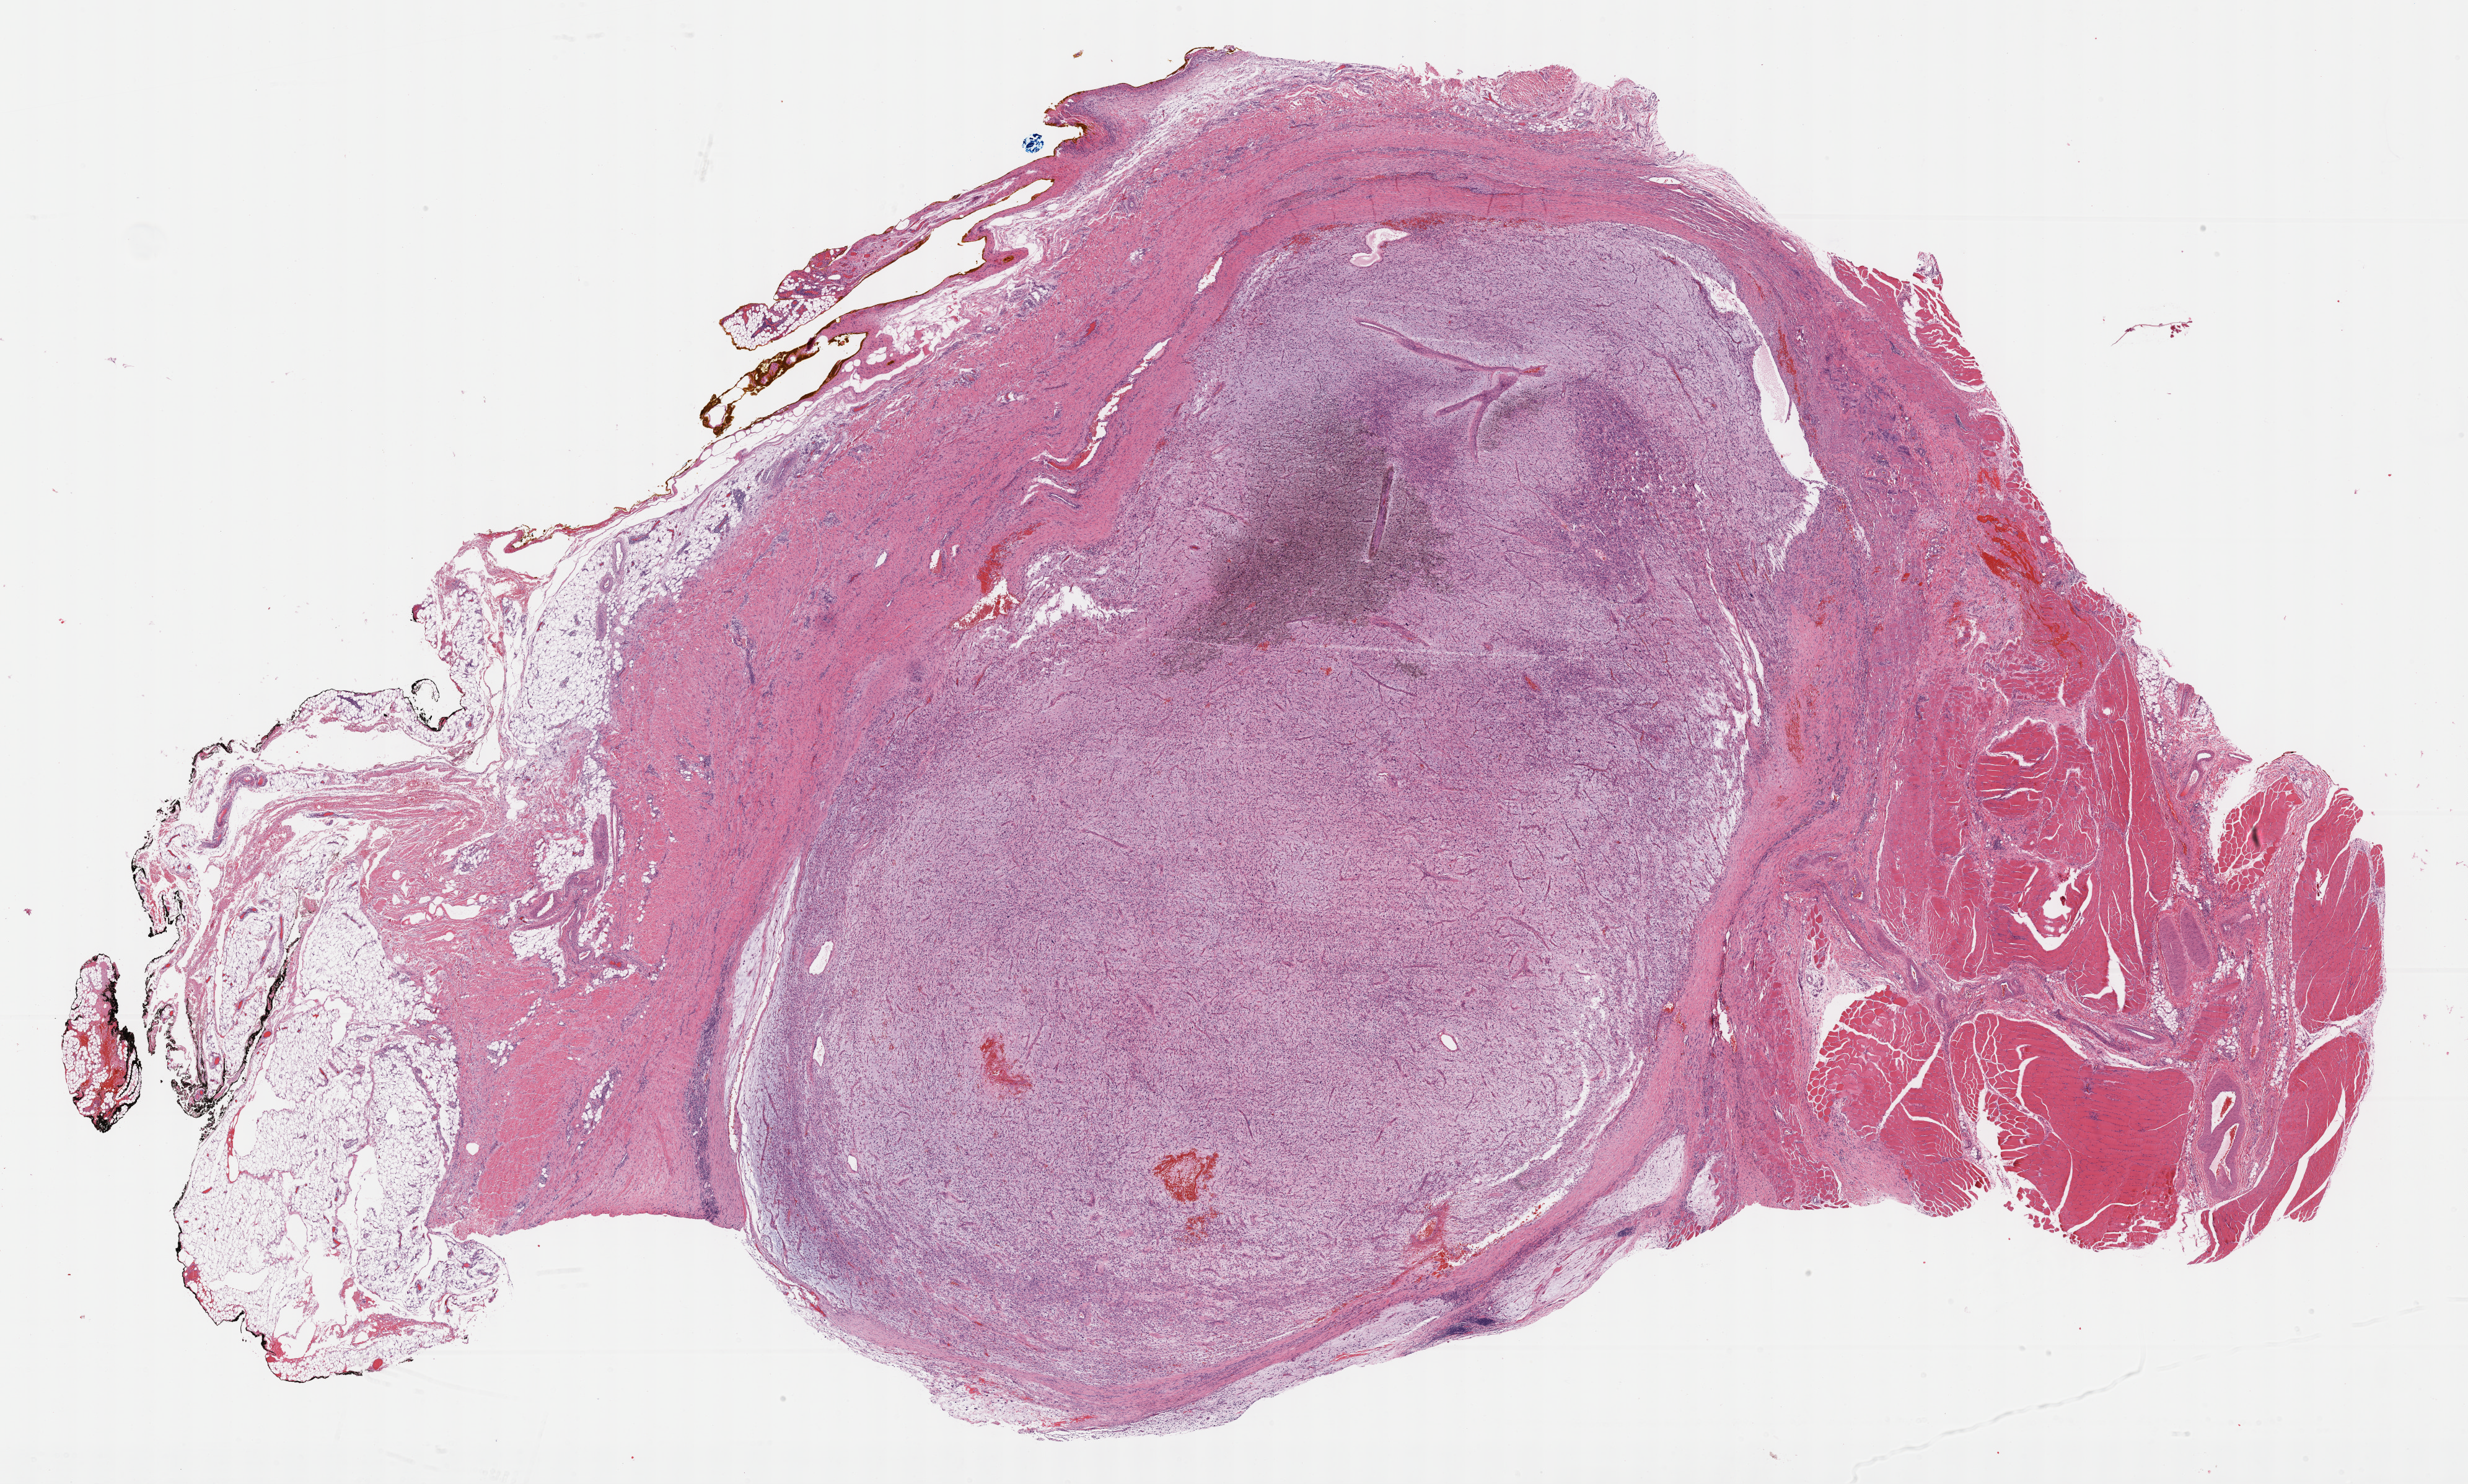
Whole-slide histology image, Hematoxylin and eosin (H&E) stained, whole scanned area (about 32.2 x 19.4 mm) shown as a low-resolution overview, FFPE section, connective, subcutaneous and other soft tissues, primary tumour sample. Patient: male, age at initial diagnosis 35 years.
Histologic diagnosis: Fibromyxosarcoma (connective, subcutaneous and other soft tissues of lower limb and hip).